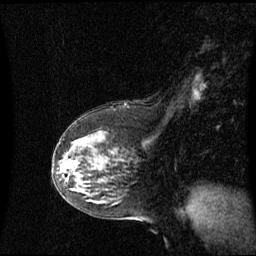
Breast MRI (dynamic contrast-enhanced), one sagittal slice. Slice 36 of 60 in the series (ordered by position). Dynamic contrast-enhanced series, image 2 of 3 at this slice position (ordered by acquisition). 1.5 T. TE 4.2 ms, TR 8.4 ms. 256 × 256 image matrix, field of view 260 × 260 mm. Patient: female, 59 years. From the clinical record (not read from this slice): setting: breast cancer imaged before/during neoadjuvant chemotherapy; receptor status: HR-positive, HER2-negative.
Outlined on this slice (semi-automatically segmented with operator editing):
- analysis volume of interest (the breast-tissue region the enhancement analysis was run in; not a lesion): bounding box [x1, y1, x2, y2] px = [61, 153, 85, 191]
- tumour enhancement mask (voxels above the 70 % enhancement threshold inside the analysis volume of interest): [70, 163, 74, 166]